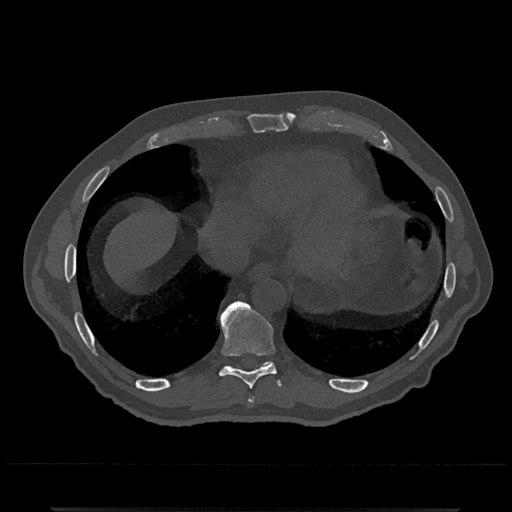
CT including the spine, one axial slice; slice 604 of 797 in the series (ordered by position); bone window (W 1800 / L 400 HU); 512 × 512 image matrix, field of view 393 × 393 mm. Patient: male, 67 years. From the clinical record (not read from this slice): primary cancer: prostate.
Structures marked on this image (semi-automatic segmentation, software-assisted and operator-edited):
- T10 vertebra: box from (x=263, y=362) to (x=270, y=365) px
- T8 vertebra: (x=249, y=397)–(x=254, y=402)
- T9 vertebra: (x=220, y=301)–(x=280, y=389)